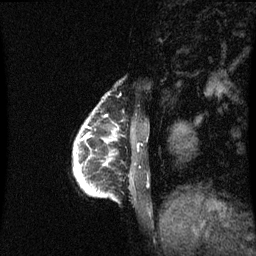
Breast MRI (dynamic contrast-enhanced), one sagittal slice; position 12 of 60 along the scan axis; dynamic contrast-enhanced series, image 2 of 3 at this slice position (ordered by acquisition); 1.5 T; TE 4.2 ms, TR 8.9 ms; 2 mm slice thickness; 256 × 256 image matrix, field of view 200 × 200 mm. Patient: female, 35 years. From the clinical record (not read from this slice): setting: breast cancer imaged before/during neoadjuvant chemotherapy; receptor status: HR-positive, HER2-negative.
Annotated regions visible in this slice (semi-automatically segmented with operator editing):
- analysis volume of interest (the breast-tissue region the enhancement analysis was run in; not a lesion): bounding box [x1, y1, x2, y2] px = [74, 118, 117, 197]
- tumour enhancement mask (voxels above the 70 % enhancement threshold inside the analysis volume of interest): [78, 174, 82, 185]